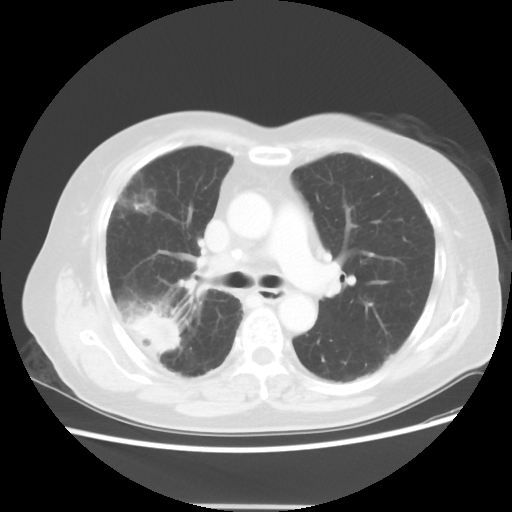
Chest CT, one axial slice; position 30 of 50 along the scan axis; 120 kVp; lung window (W 1500 / L -600 HU); 5 mm slice thickness; 512 × 512 image matrix, field of view 360 × 360 mm. Patient: female, 72 years. From the clinical record (not read from this slice): clinical TNM (as recorded): T2 N1 M0; histopathological grade: G1.
Annotated regions visible in this slice (rectangle marked by the reading radiologist):
- lung tumour (recorded histology: adenocarcinoma): bounding box (x1, y1, x2, y2) in pixels: (125, 307, 180, 354)